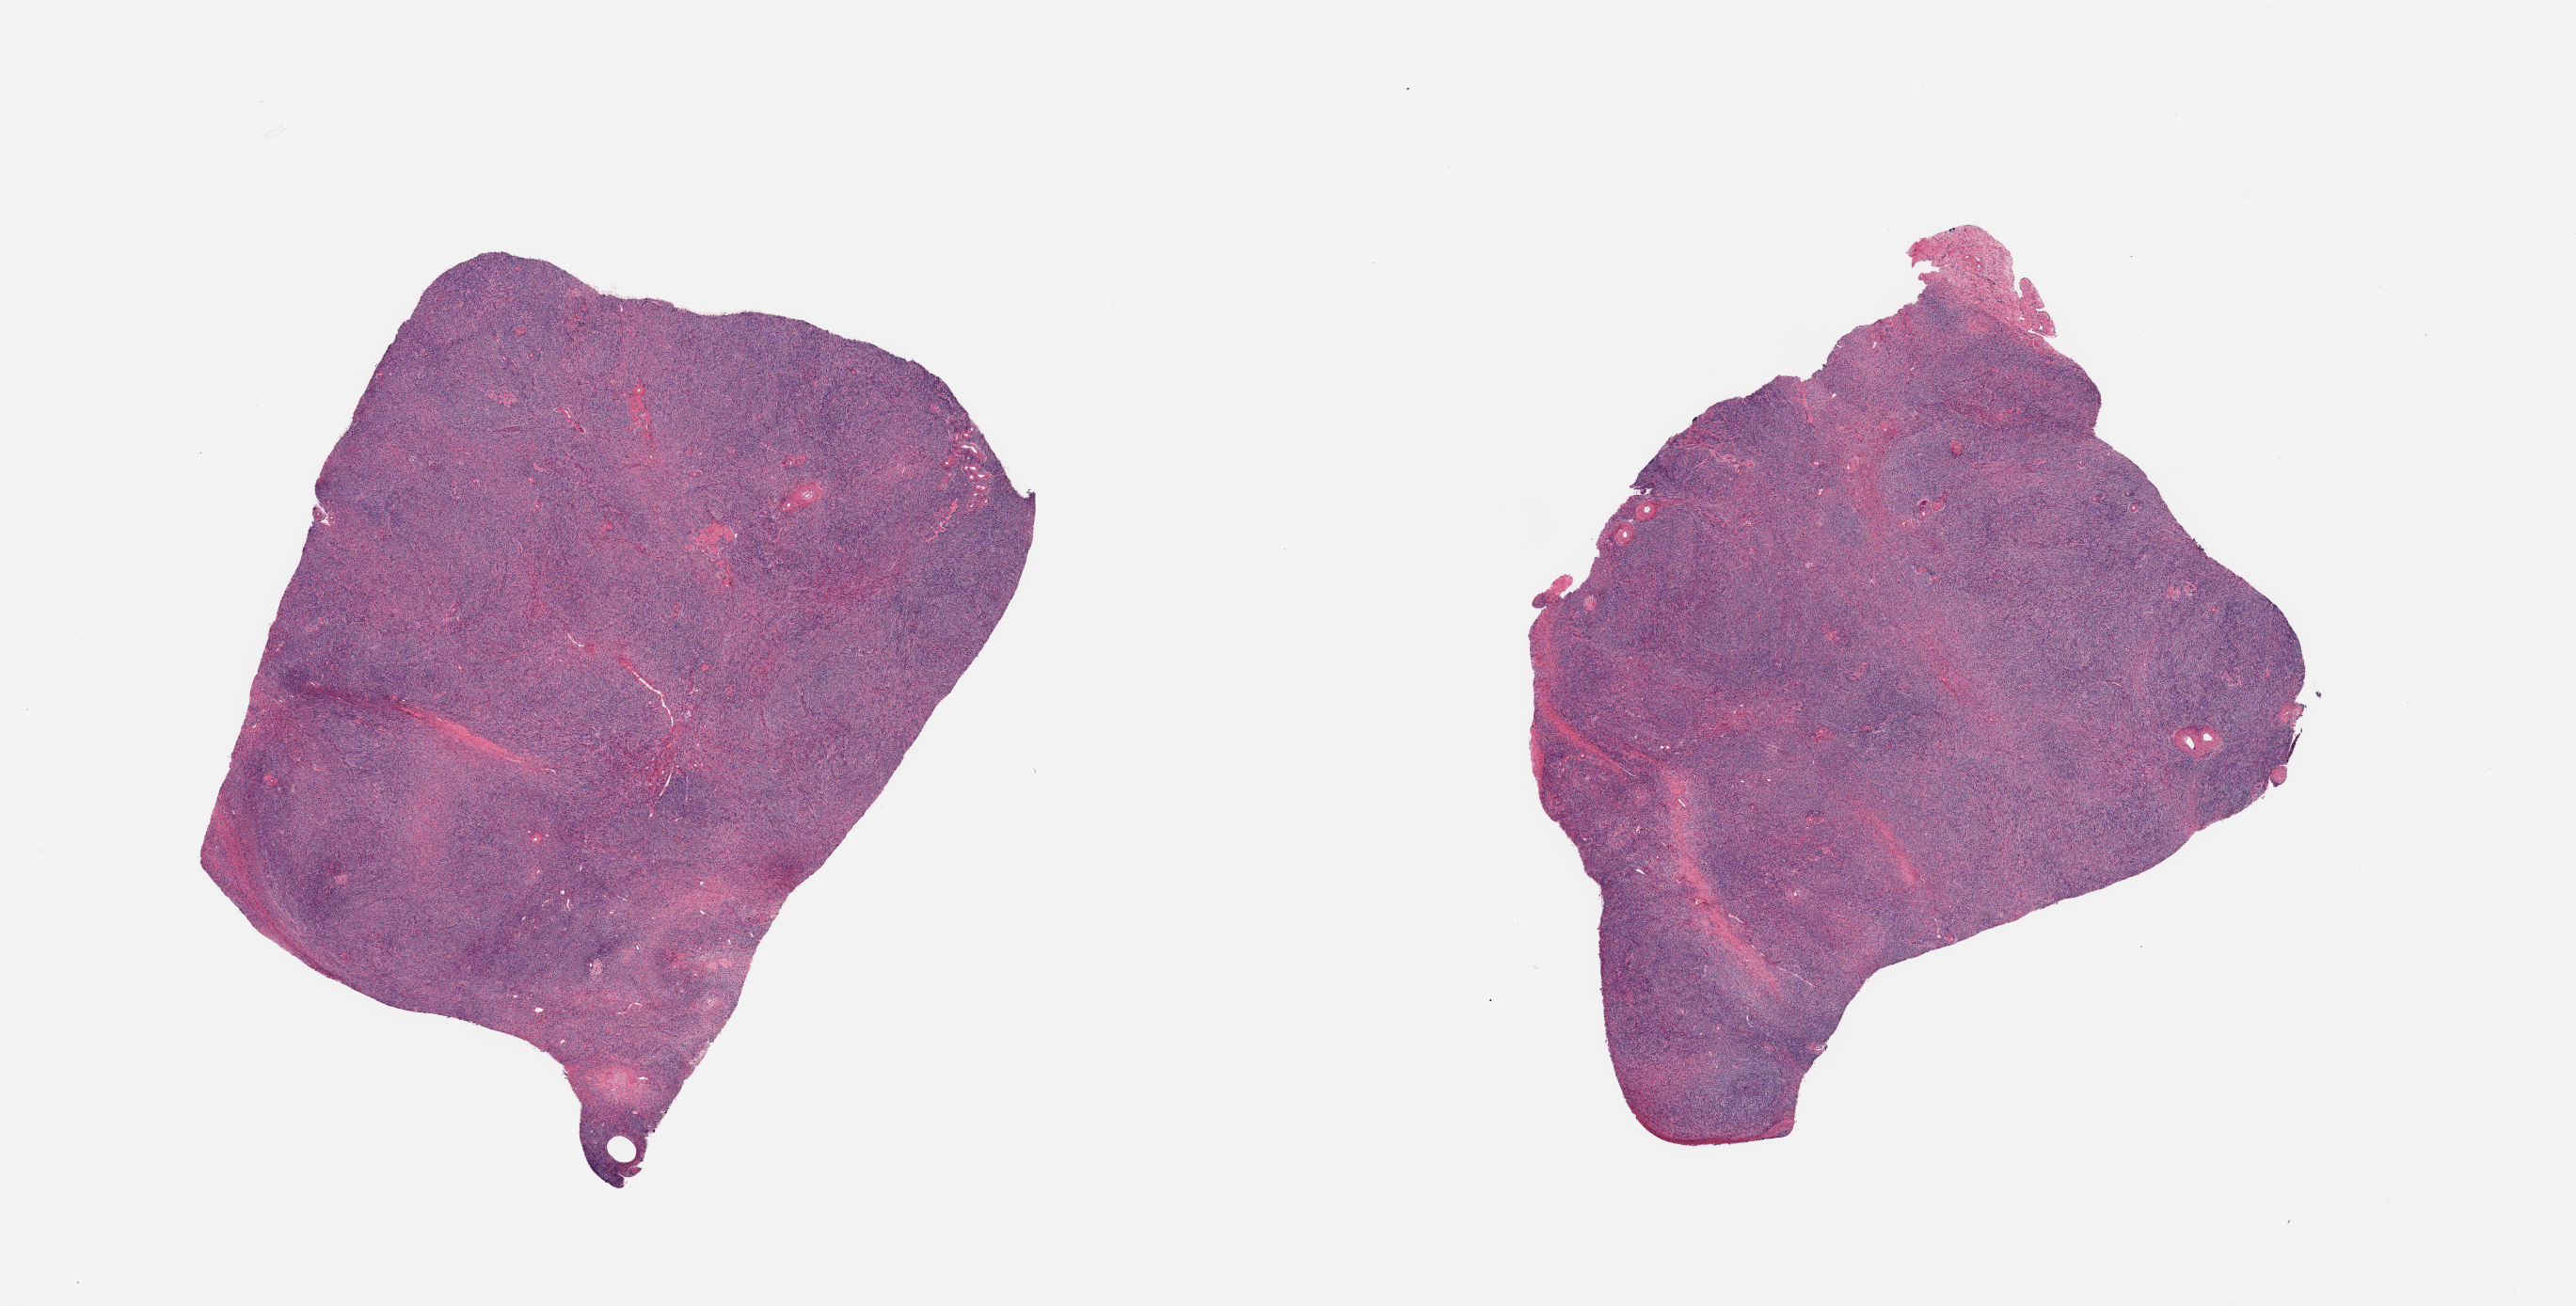
H&E whole-slide image, brightfield, whole scanned area (about 21.7 x 11.0 mm, from a 20x scan) shown as a low-resolution overview; PAXgene-fixed, paraffin-embedded tissue; section of ovary (target tissue); donor tissue sample.
Review note (as recorded): 2 pieces, post menopausal atrophy.